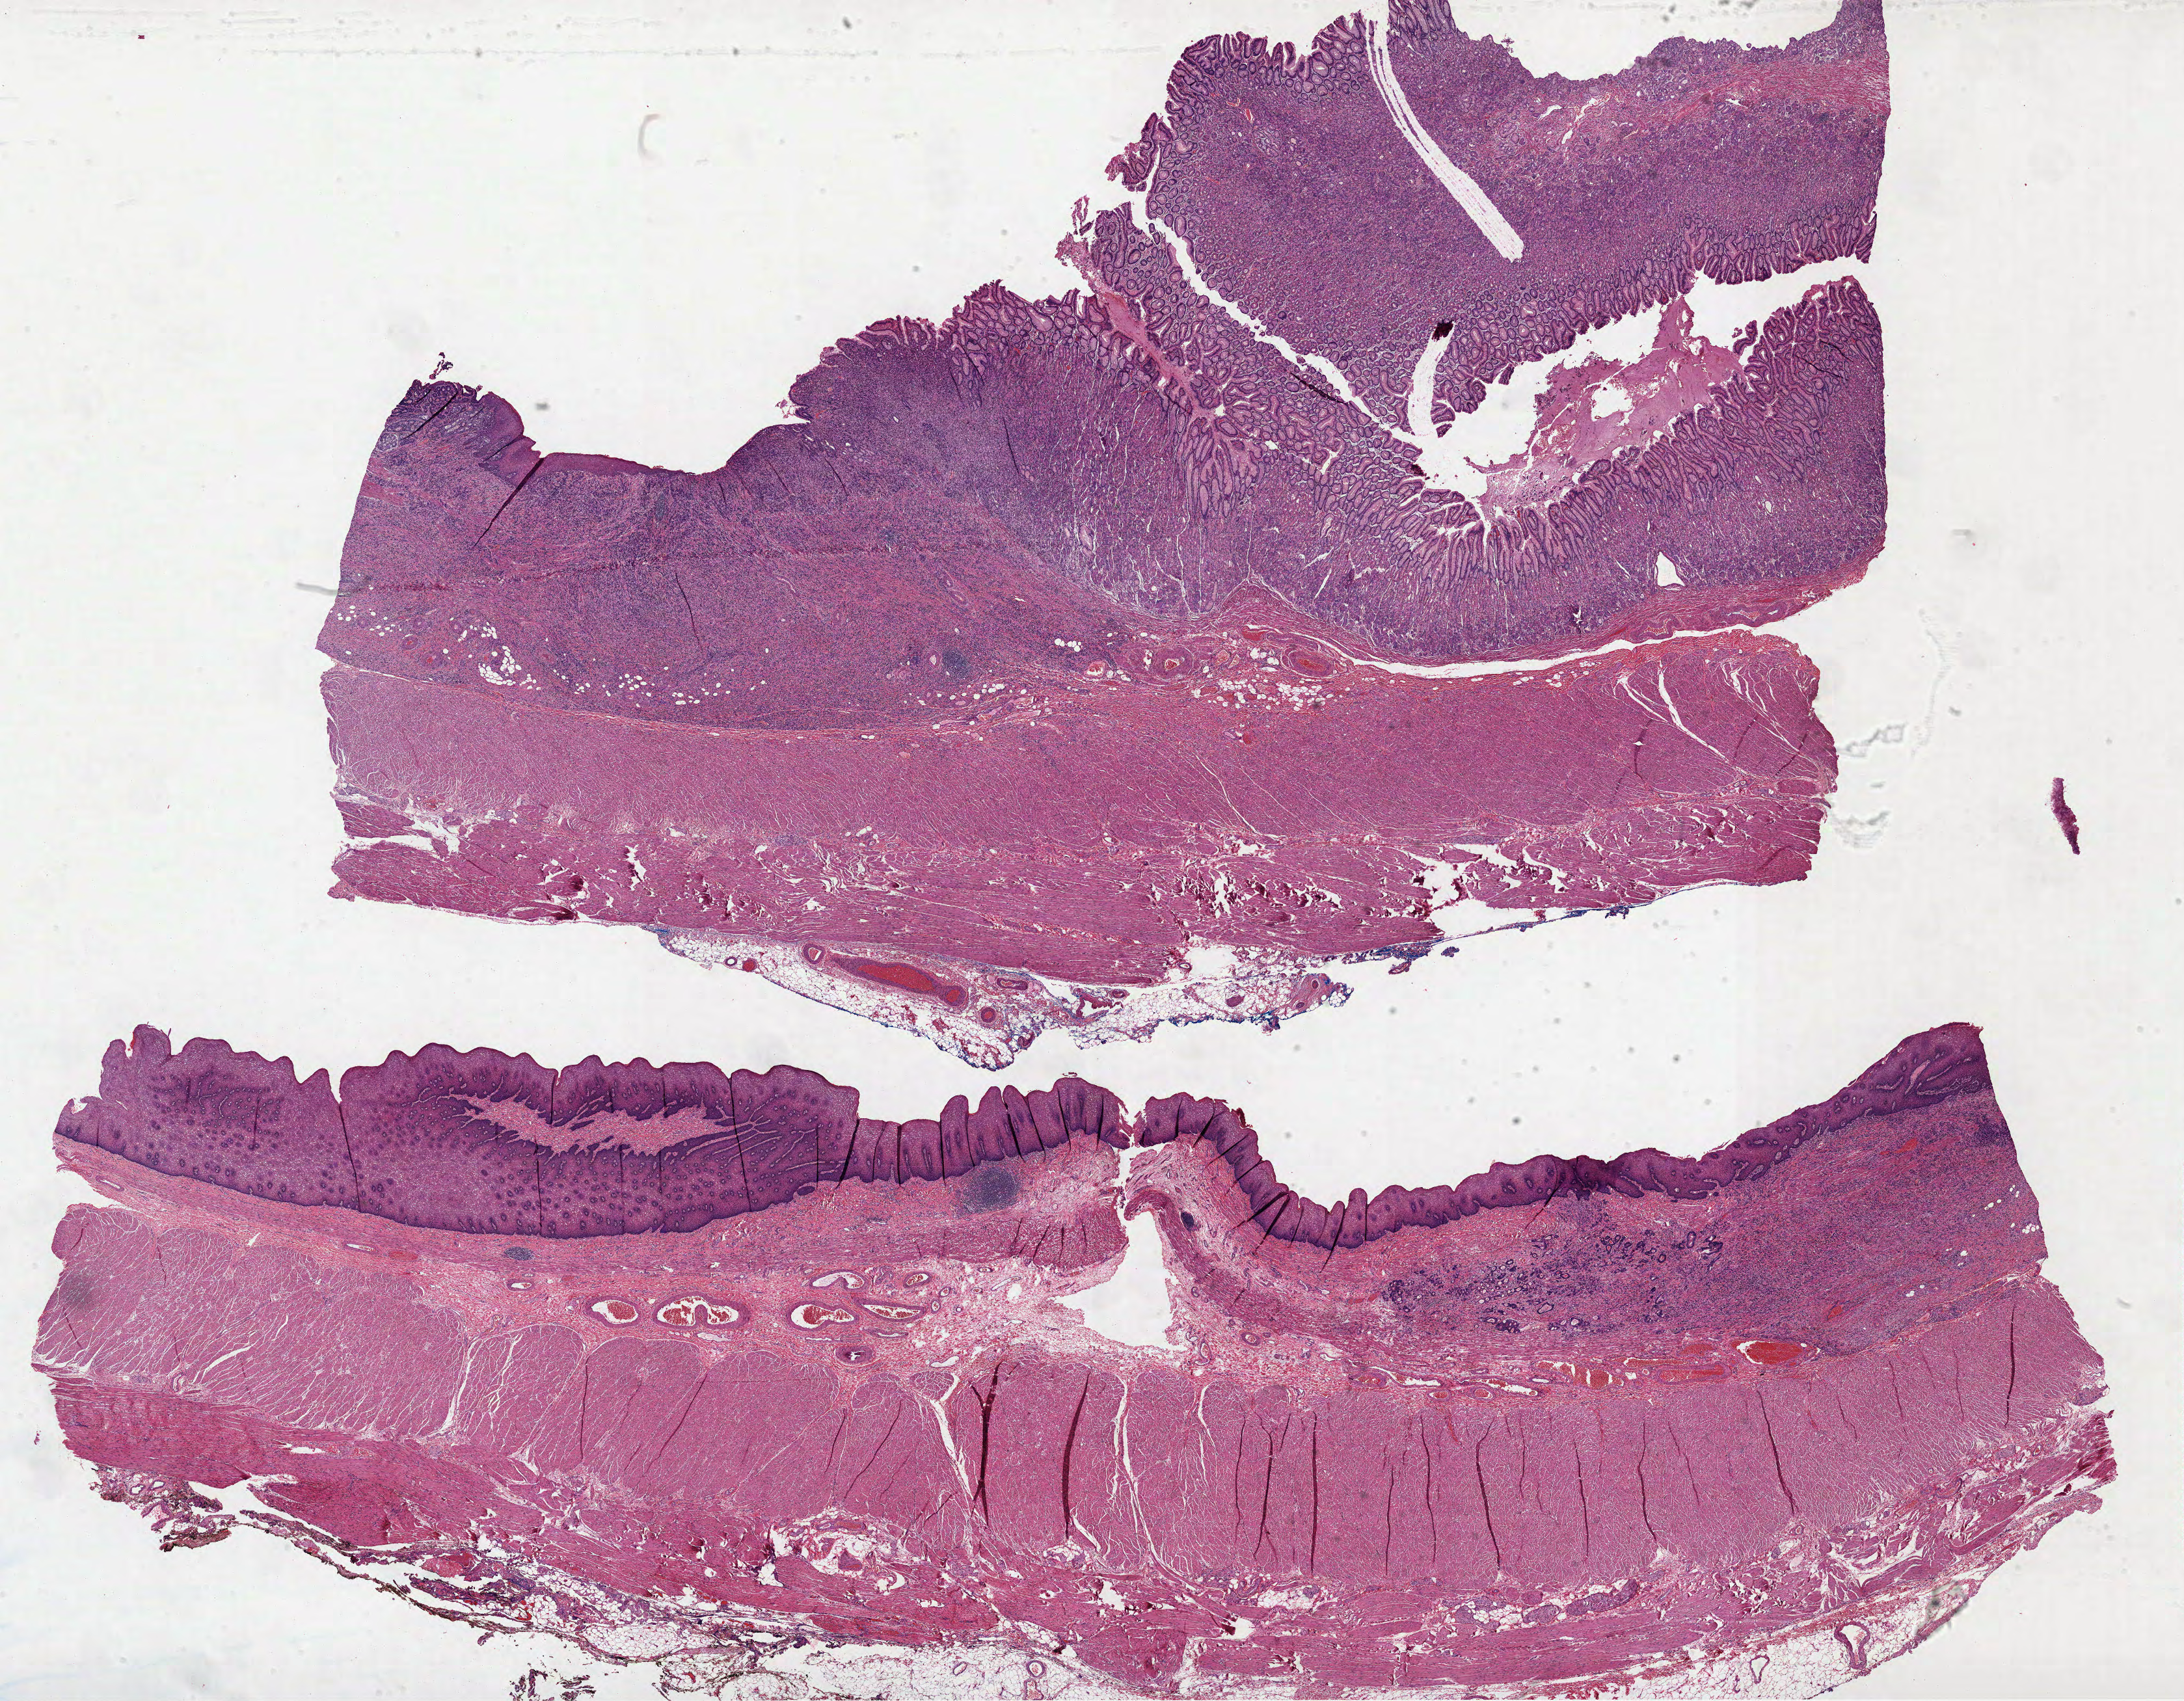
Whole-slide histology image, H&E — low-resolution overview of the scanned area, about 27.1 x 21.1 mm (acquisition: 40x scan). Formalin-fixed paraffin-embedded (FFPE) diagnostic section. Stomach, primary tumour sample. Male, age 50 years at initial diagnosis. Histologic grade: G3 (poorly differentiated).
* histologic diagnosis: Carcinoma, diffuse type (cardia, NOS)
* AJCC pathologic stage: IIB (7th edition)
* TNM: T3 N1 M0
* lymph nodes positive (case pathology): 2 of 17 examined